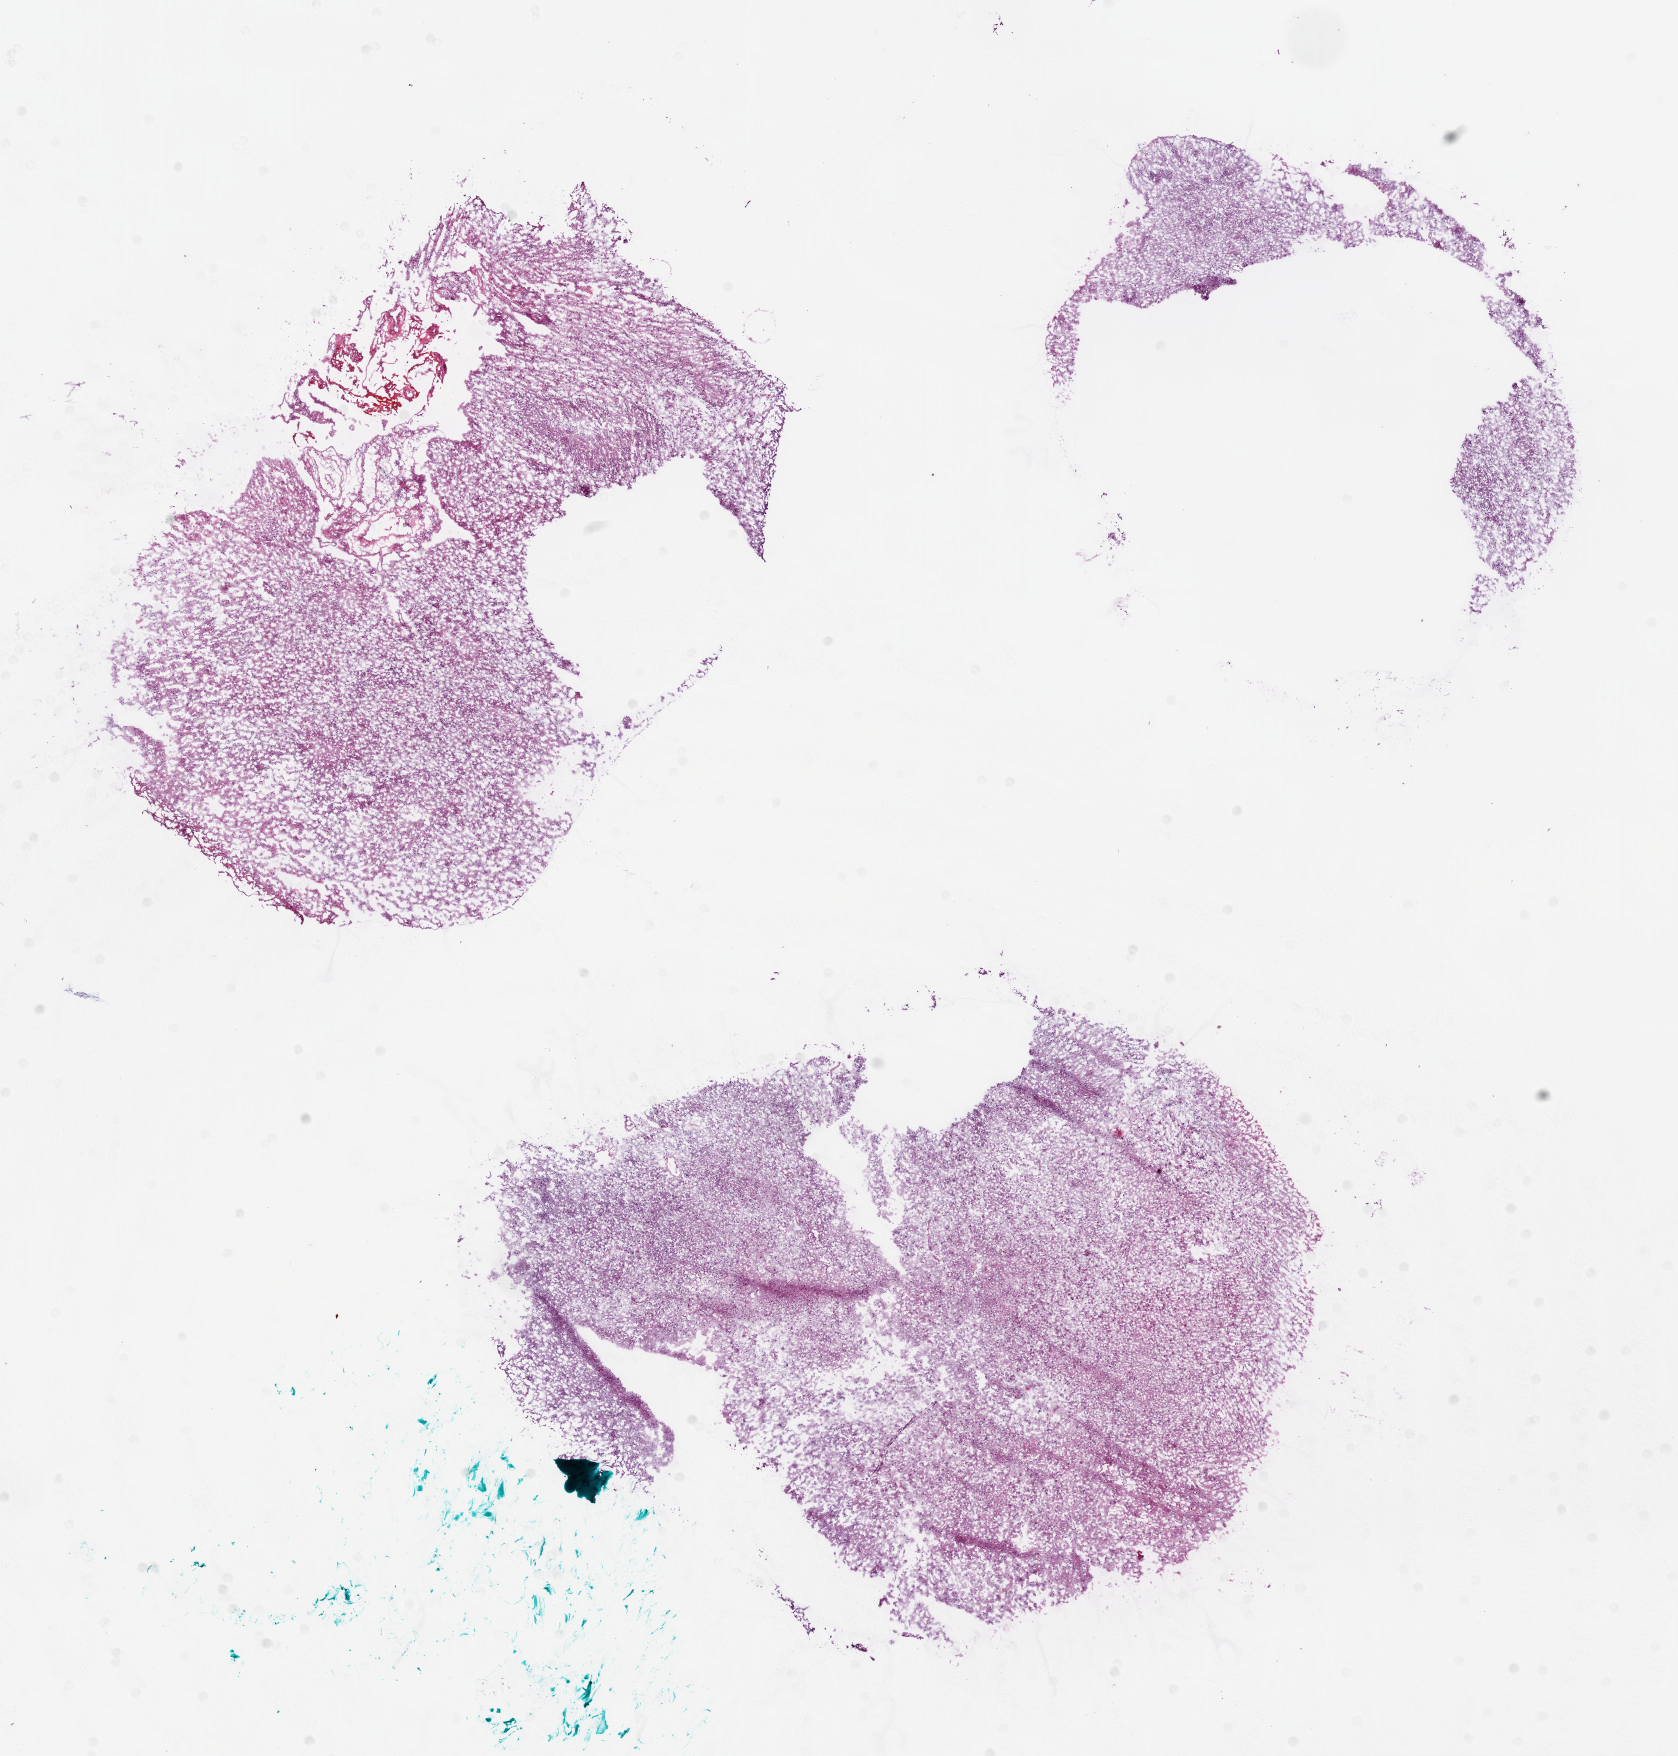
Whole-slide histology image, H&E — shown as a low-resolution overview of the whole scanned area (about 13.5 x 14.2 mm), frozen section from the bottom of the tissue portion, sample: primary tumour, brain. Male patient; age at initial diagnosis 65 years. Pathologist review of this section (percent, as recorded): tumour cells 85%, tumour nuclei 90%, stromal cells 5%, necrosis 10%.
- histologic diagnosis: Glioblastoma